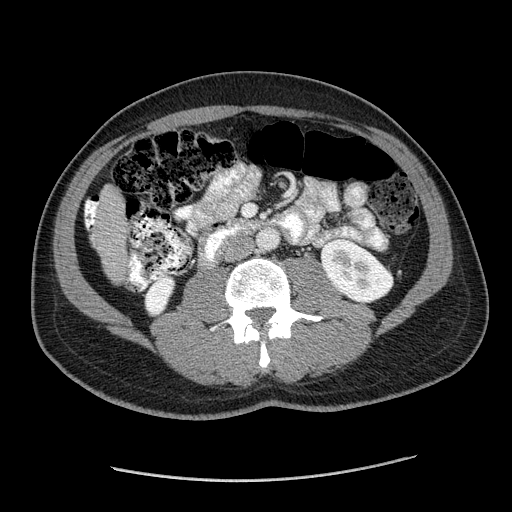
Contrast-enhanced abdominal CT (liver protocol), one axial slice. Position 33 of 182 along the scan axis. Reconstruction kernel STANDARD. 120 kVp. Soft-tissue window (W 400 / L 40 HU). 512 × 512 image matrix, field of view 400 × 400 mm. Case-level facts recorded for this patient, not image findings: diagnosis: hepatocellular carcinoma (patient treated with transarterial chemoembolisation; whether this scan precedes or follows treatment is not stated here); TNM stage (as recorded): Stage-I; Child-Pugh class: A; tumour size: 3.1 cm.
Structures marked on this image (semi-automatic segmentation, software-assisted and operator-edited):
- liver parenchyma outside the tumour (the mass and vessels are separate outlines, so this box may not span the whole liver): bounding box (x1, y1, x2, y2) in pixels: (84, 184, 128, 282)
- liver vessels: (85, 201, 98, 227)